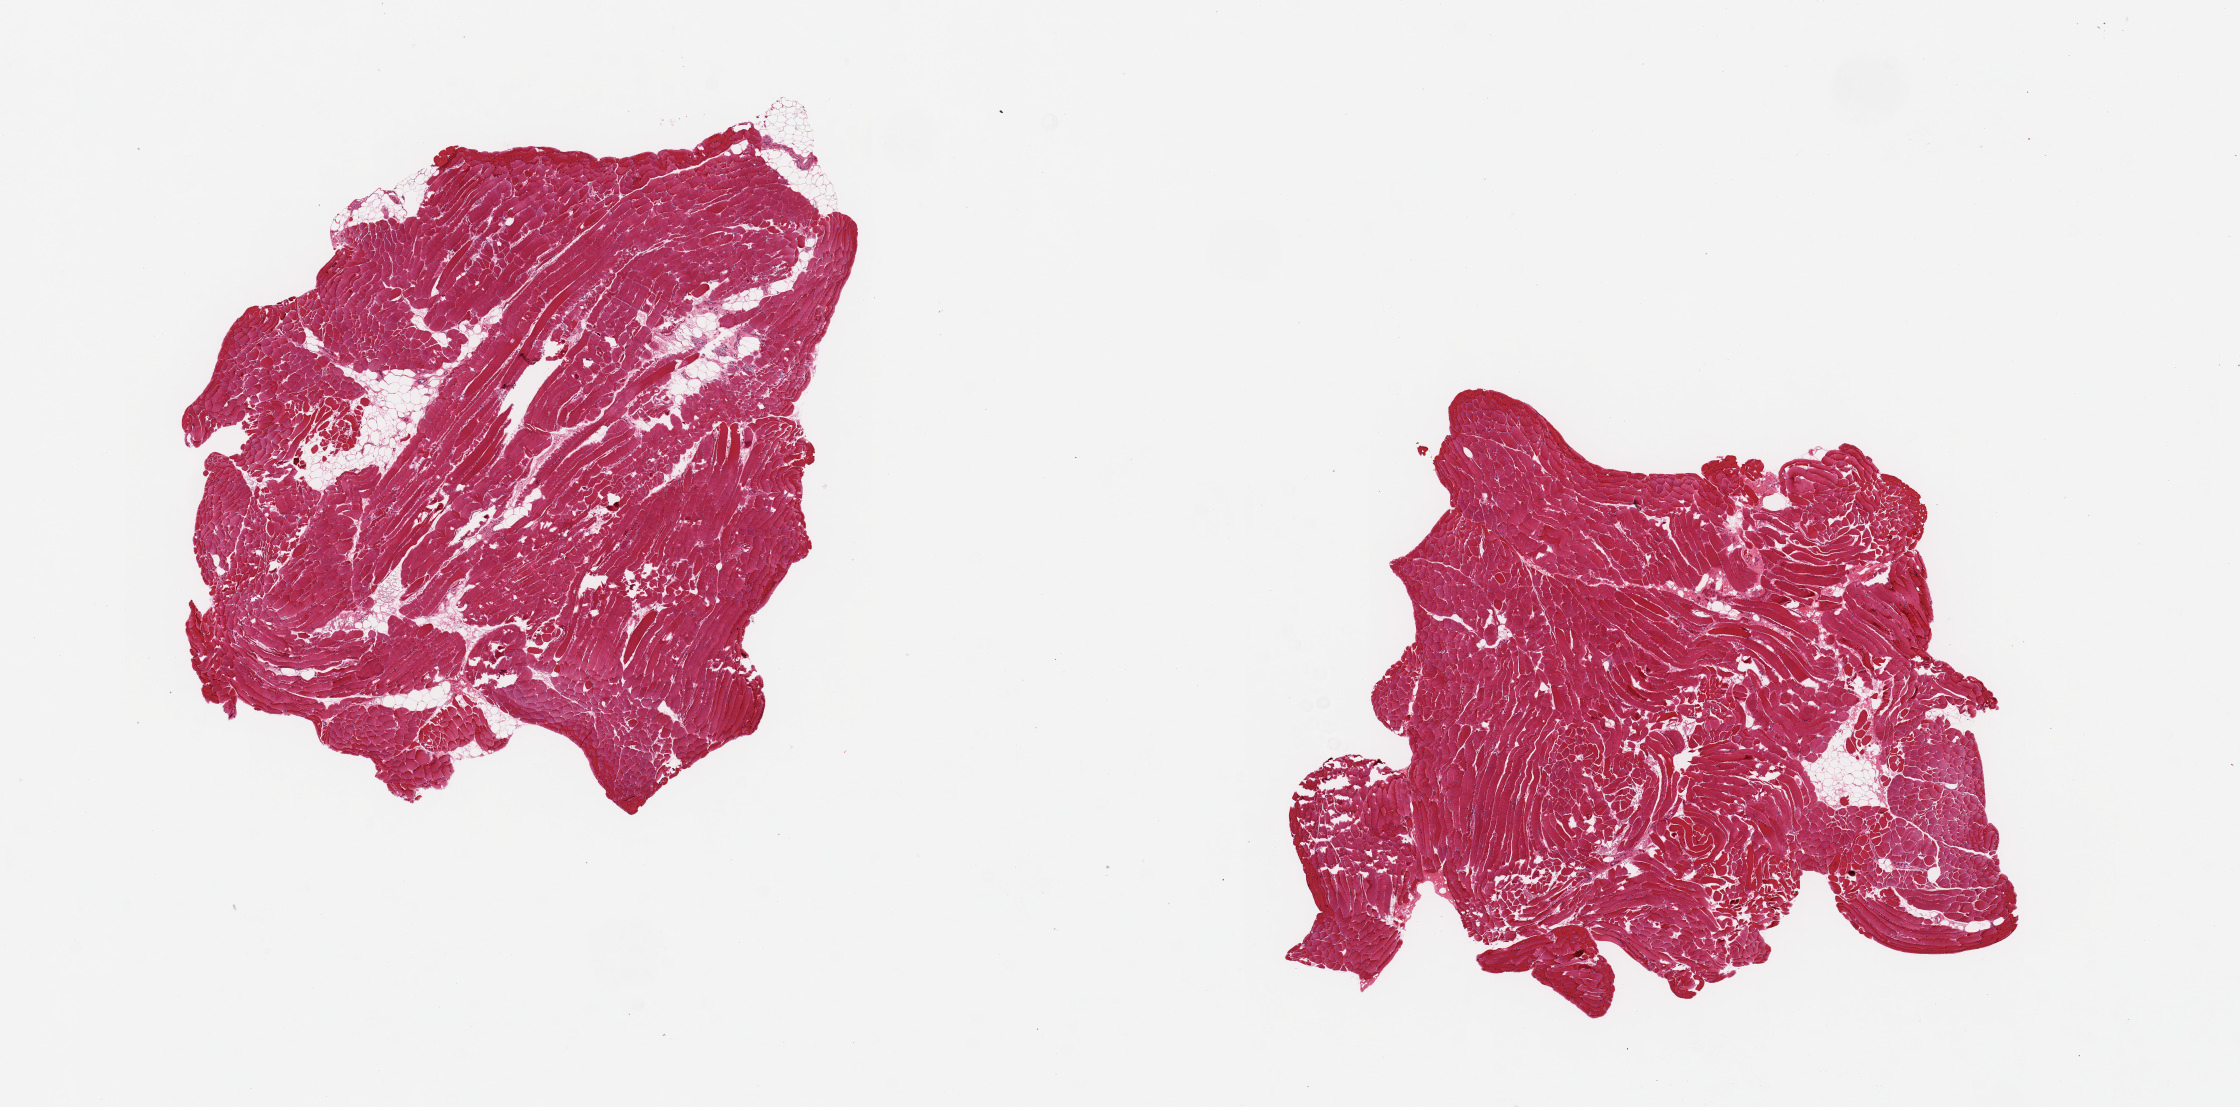
Digitized haematoxylin and eosin-stained section — whole scanned area (about 17.7 x 8.8 mm, slide scanned at 20x) shown as a low-resolution overview. PAXgene-fixed paraffin-embedded (PFPE) section. Sampled site (target tissue): skeletal muscle. Donor tissue sample. Male donor.
- pathologist's review note for this sample: 2 pieces ~6x6mm, interstitial fat is ~10-20% of specimens